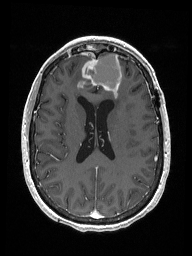
Brain MRI from a brain-tumour surgery series, one axial slice; position 71 of 192 along the scan axis; T1-weighted post-contrast; 1 mm slice thickness; 192 × 256 image matrix, field of view 187 × 250 mm. Case-level facts recorded for this patient, not image findings: histopathology: Metastastic Carcinoma from Breast primary; tumour location: Right Frontal.
Outlined on this slice (manually delineated by an expert):
- previous resection cavity: bounding box <86,52,122,95> (left, top, right, bottom; pixels)